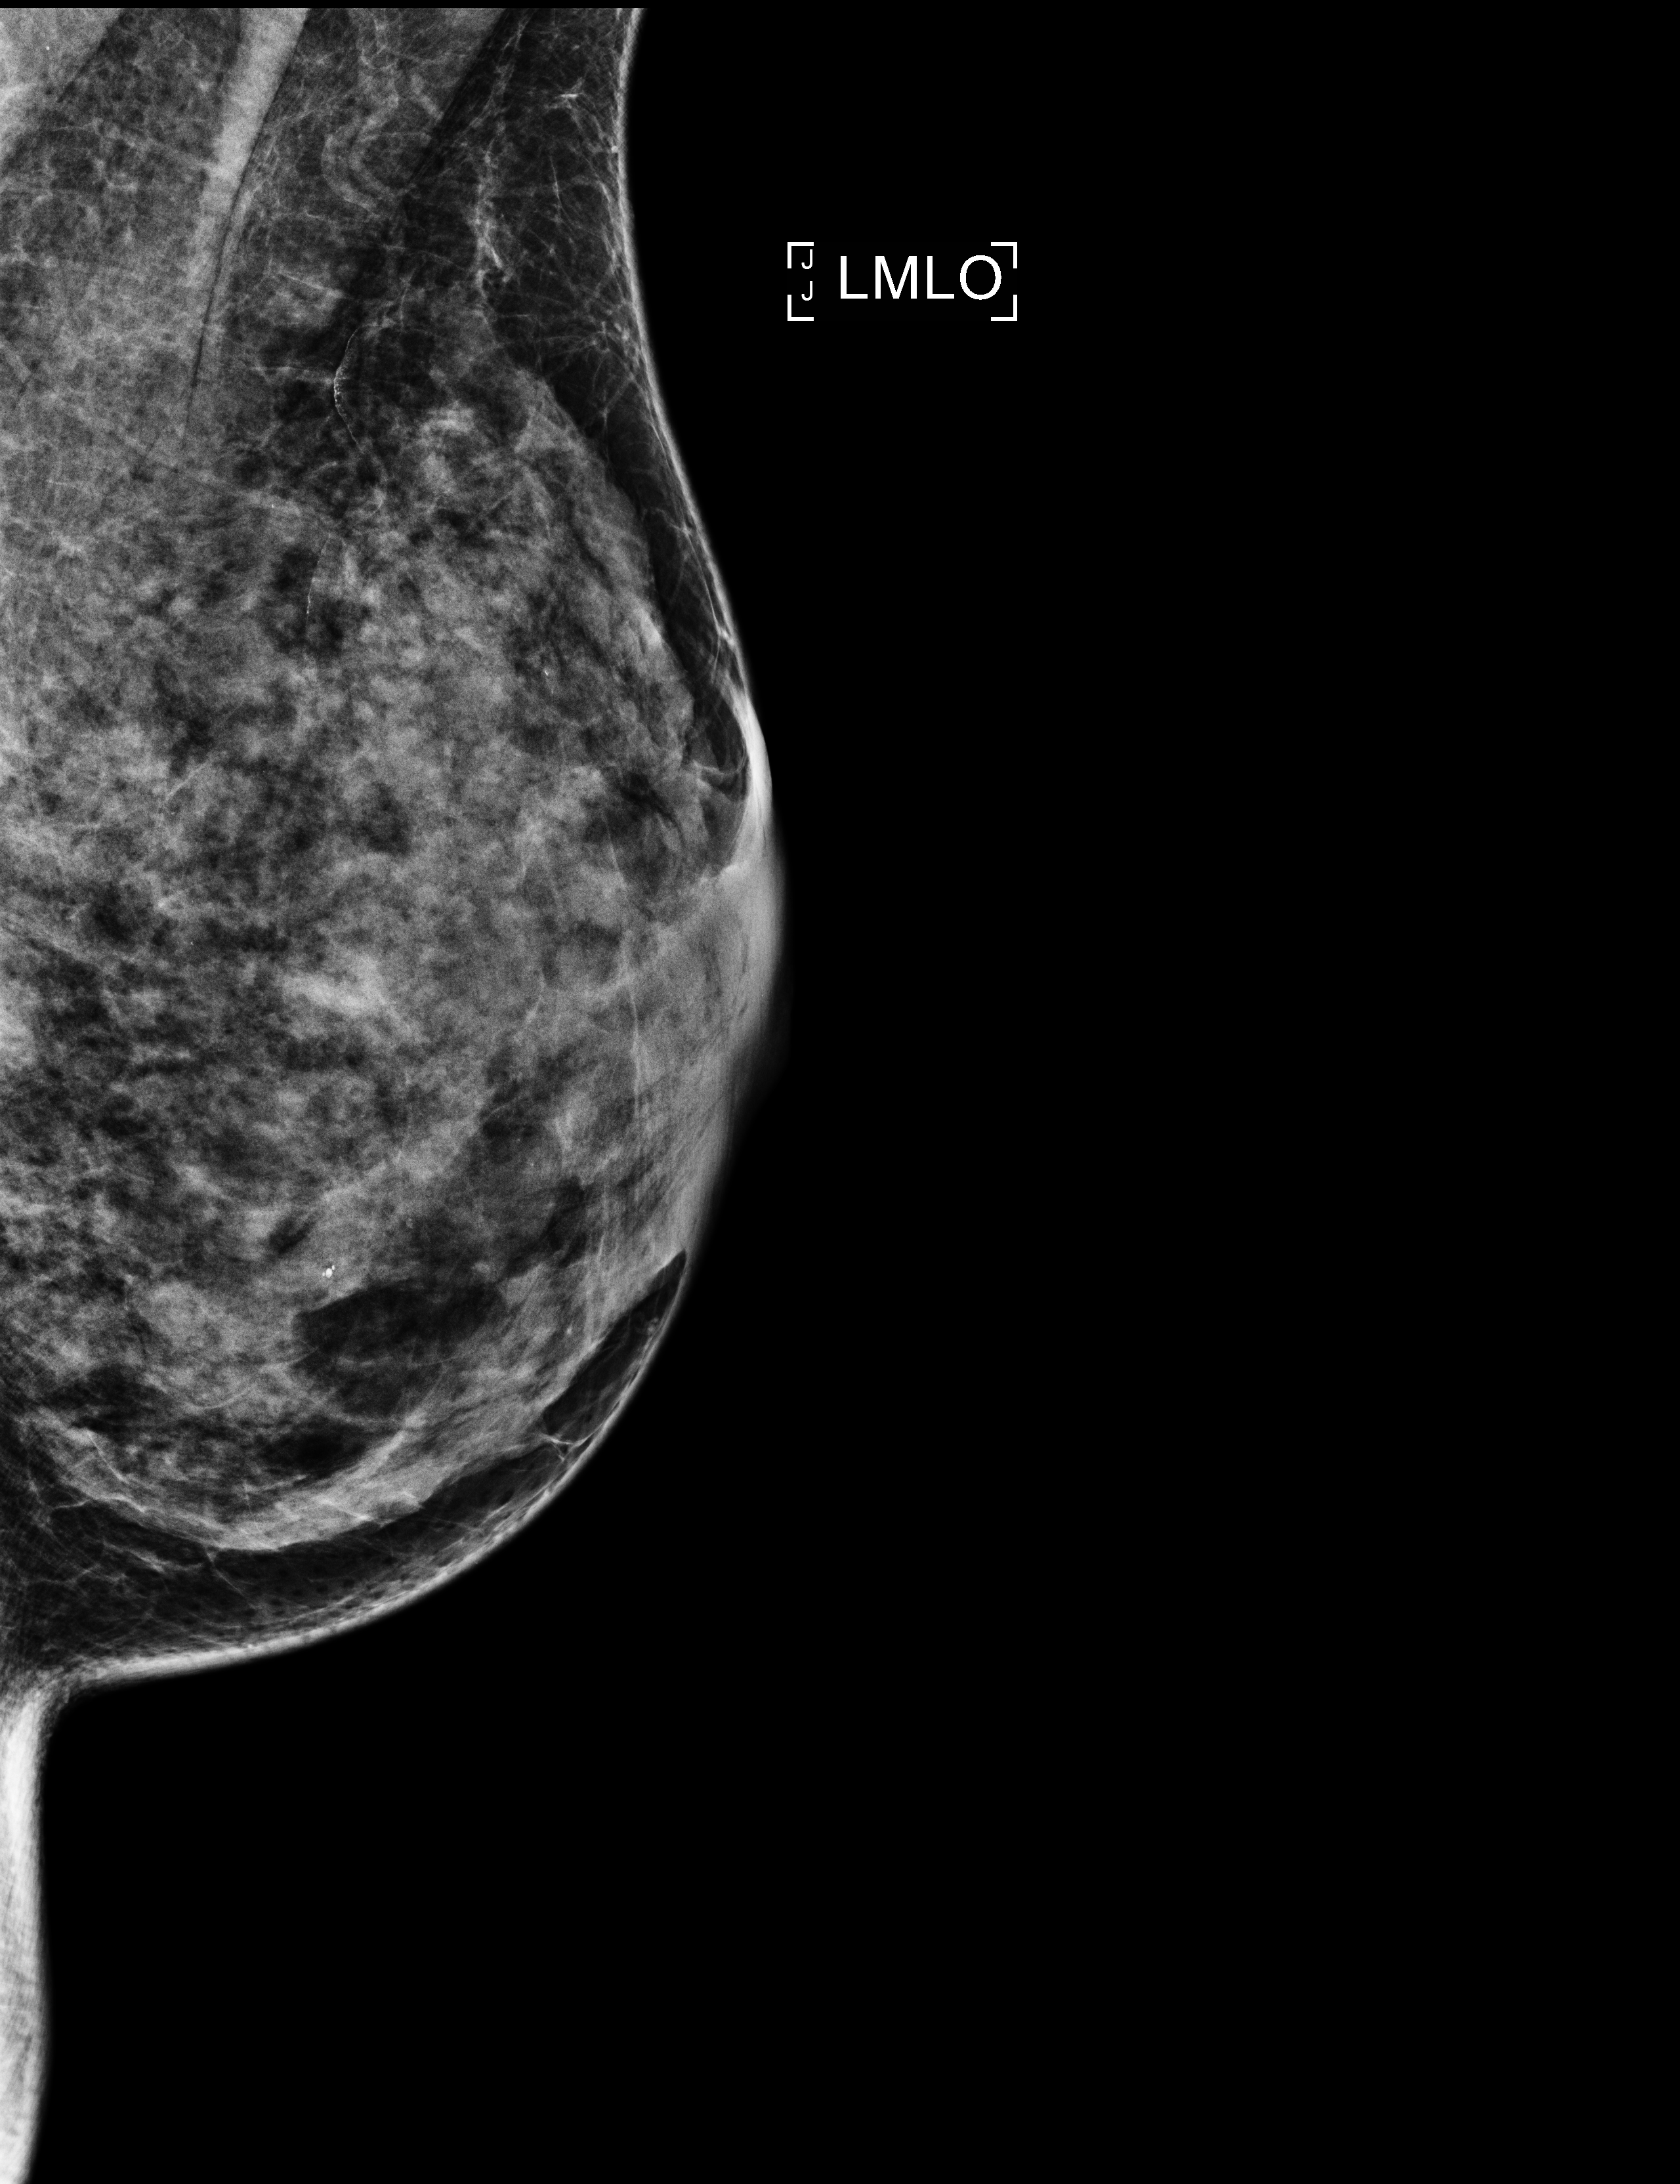
Digital mammogram (FFDM), left breast, MLO view, annual screening mammography examination. Patient aged 56 years (female).
- breast density at the screening exam (both breasts): almost entirely fatty (BI-RADS density category a)
- final BI-RADS category for the screening round (tomosynthesis exam, both breasts): category 1
- recall: no recall after this screen